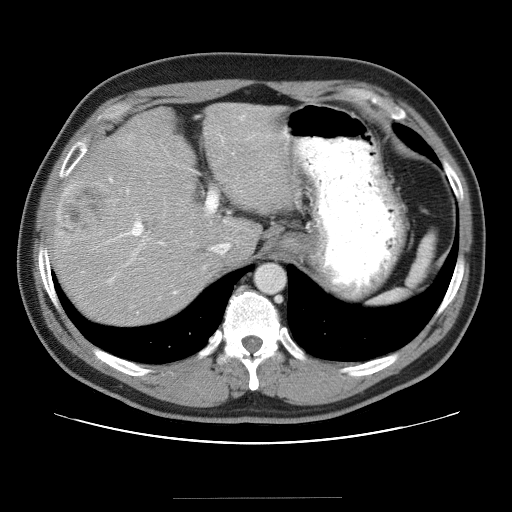
Contrast-enhanced abdominal CT (liver protocol), one axial slice; position 27 of 40 along the scan axis; reconstruction kernel STANDARD; soft-tissue window (W 400 / L 40 HU); 512 × 512 image matrix, field of view 380 × 380 mm. Case-level facts recorded for this patient, not image findings: diagnosis: hepatocellular carcinoma (patient treated with transarterial chemoembolisation; whether this scan precedes or follows treatment is not stated here); TNM stage (as recorded): Stage-IVA; Child-Pugh class: B.
Outlined on this slice (semi-automatic segmentation, software-assisted and operator-edited):
- abdominal aorta: bounding box (x1, y1, x2, y2) in pixels: (255, 264, 284, 293)
- liver parenchyma outside the tumour (the mass and vessels are separate outlines, so this box may not span the whole liver): (52, 102, 300, 324)
- mass: (55, 179, 121, 242)
- liver vessels: (109, 118, 289, 294)